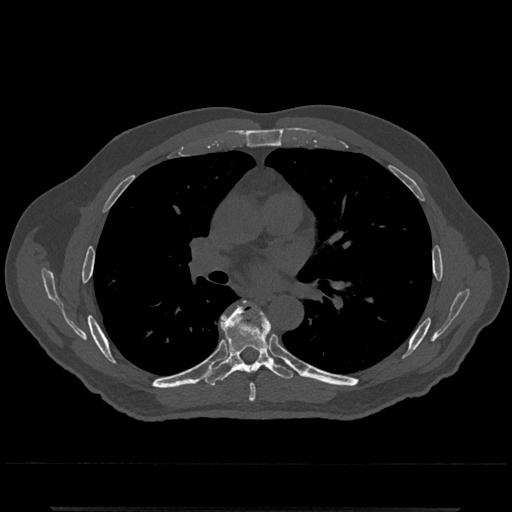
CT including the spine, one axial slice. Position 739 of 797 along the scan axis. Reconstruction kernel Br40s/3. 120 kVp. Bone window (W 1800 / L 400 HU). 0.5 mm slice thickness. 512 × 512 image matrix, field of view 393 × 393 mm. Patient: male, 67 years. From the clinical record (not read from this slice): primary cancer: prostate.
Annotated regions visible in this slice (semi-automatic segmentation, software-assisted and operator-edited):
- T6 vertebra: box from (x=249, y=384) to (x=256, y=402) px
- T7 vertebra: (x=201, y=304)–(x=294, y=386)